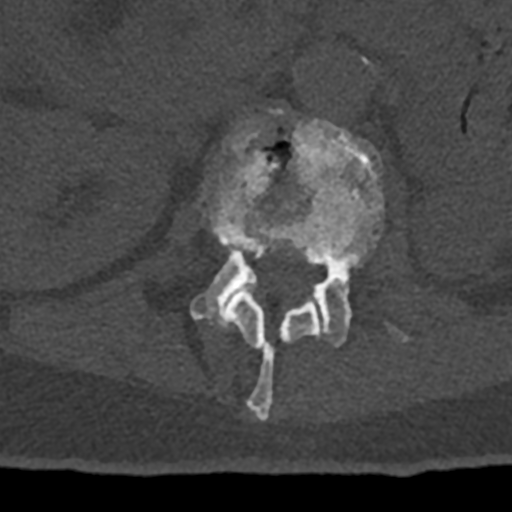
CT including the spine, one axial slice; slice 404 of 797 in the series (ordered by position); reconstruction kernel Br40s/3; 120 kVp; bone window (W 1800 / L 400 HU); 0.5 mm slice thickness; 512 × 512 image matrix, field of view 160 × 160 mm. Patient: male, 74 years. Case-level facts recorded for this patient, not image findings: primary cancer: renal.
Outlined on this slice (semi-automatic segmentation, software-assisted and operator-edited):
- L1 vertebra: bounding box (x1, y1, x2, y2) in pixels: (204, 121, 320, 421)
- L2 vertebra: (190, 110, 409, 347)